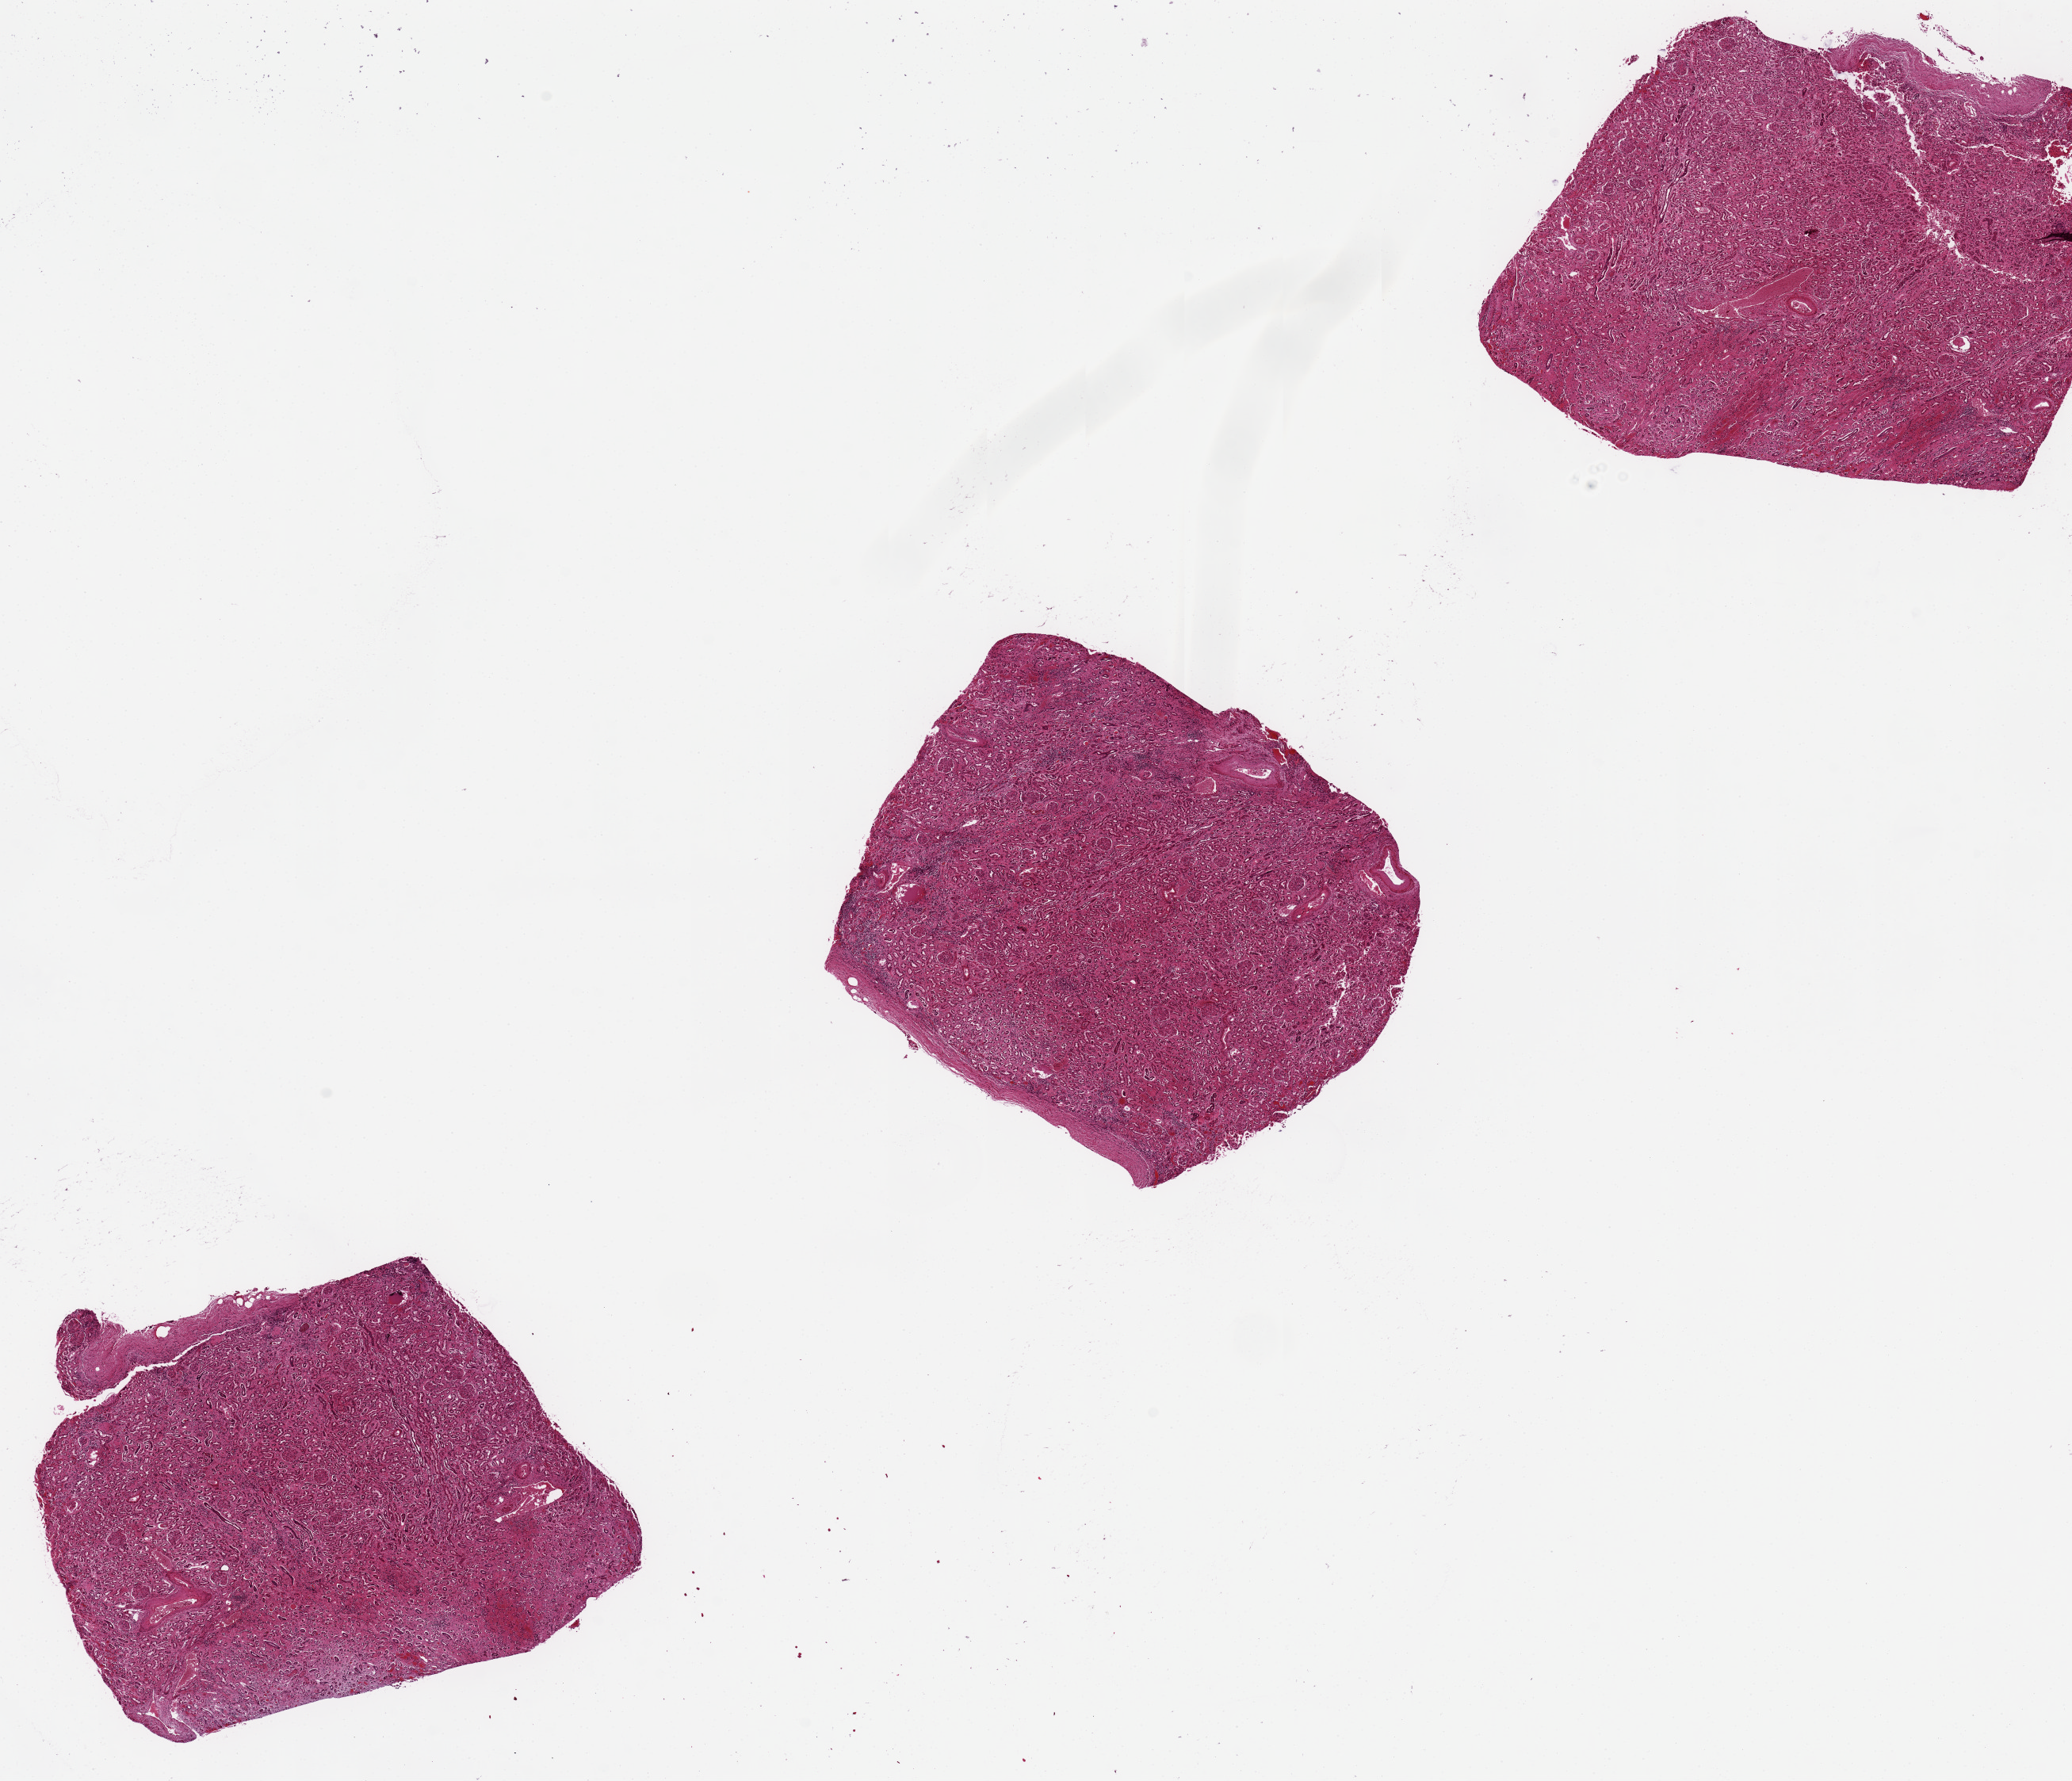
Digitized haematoxylin and eosin-stained section — a low-resolution overview of the entire scanned area, about 20.7 x 17.8 mm (slide scanned at 20x), PAXgene-fixed, paraffin-embedded tissue, target tissue: renal cortex, tissue donor sample. Female donor.
Pathologist's review note for this sample: 1 (glomeruli) to 1 (tubules). Interstital fibrosis, moderate. 3 pieces, average 5 x 6mm.